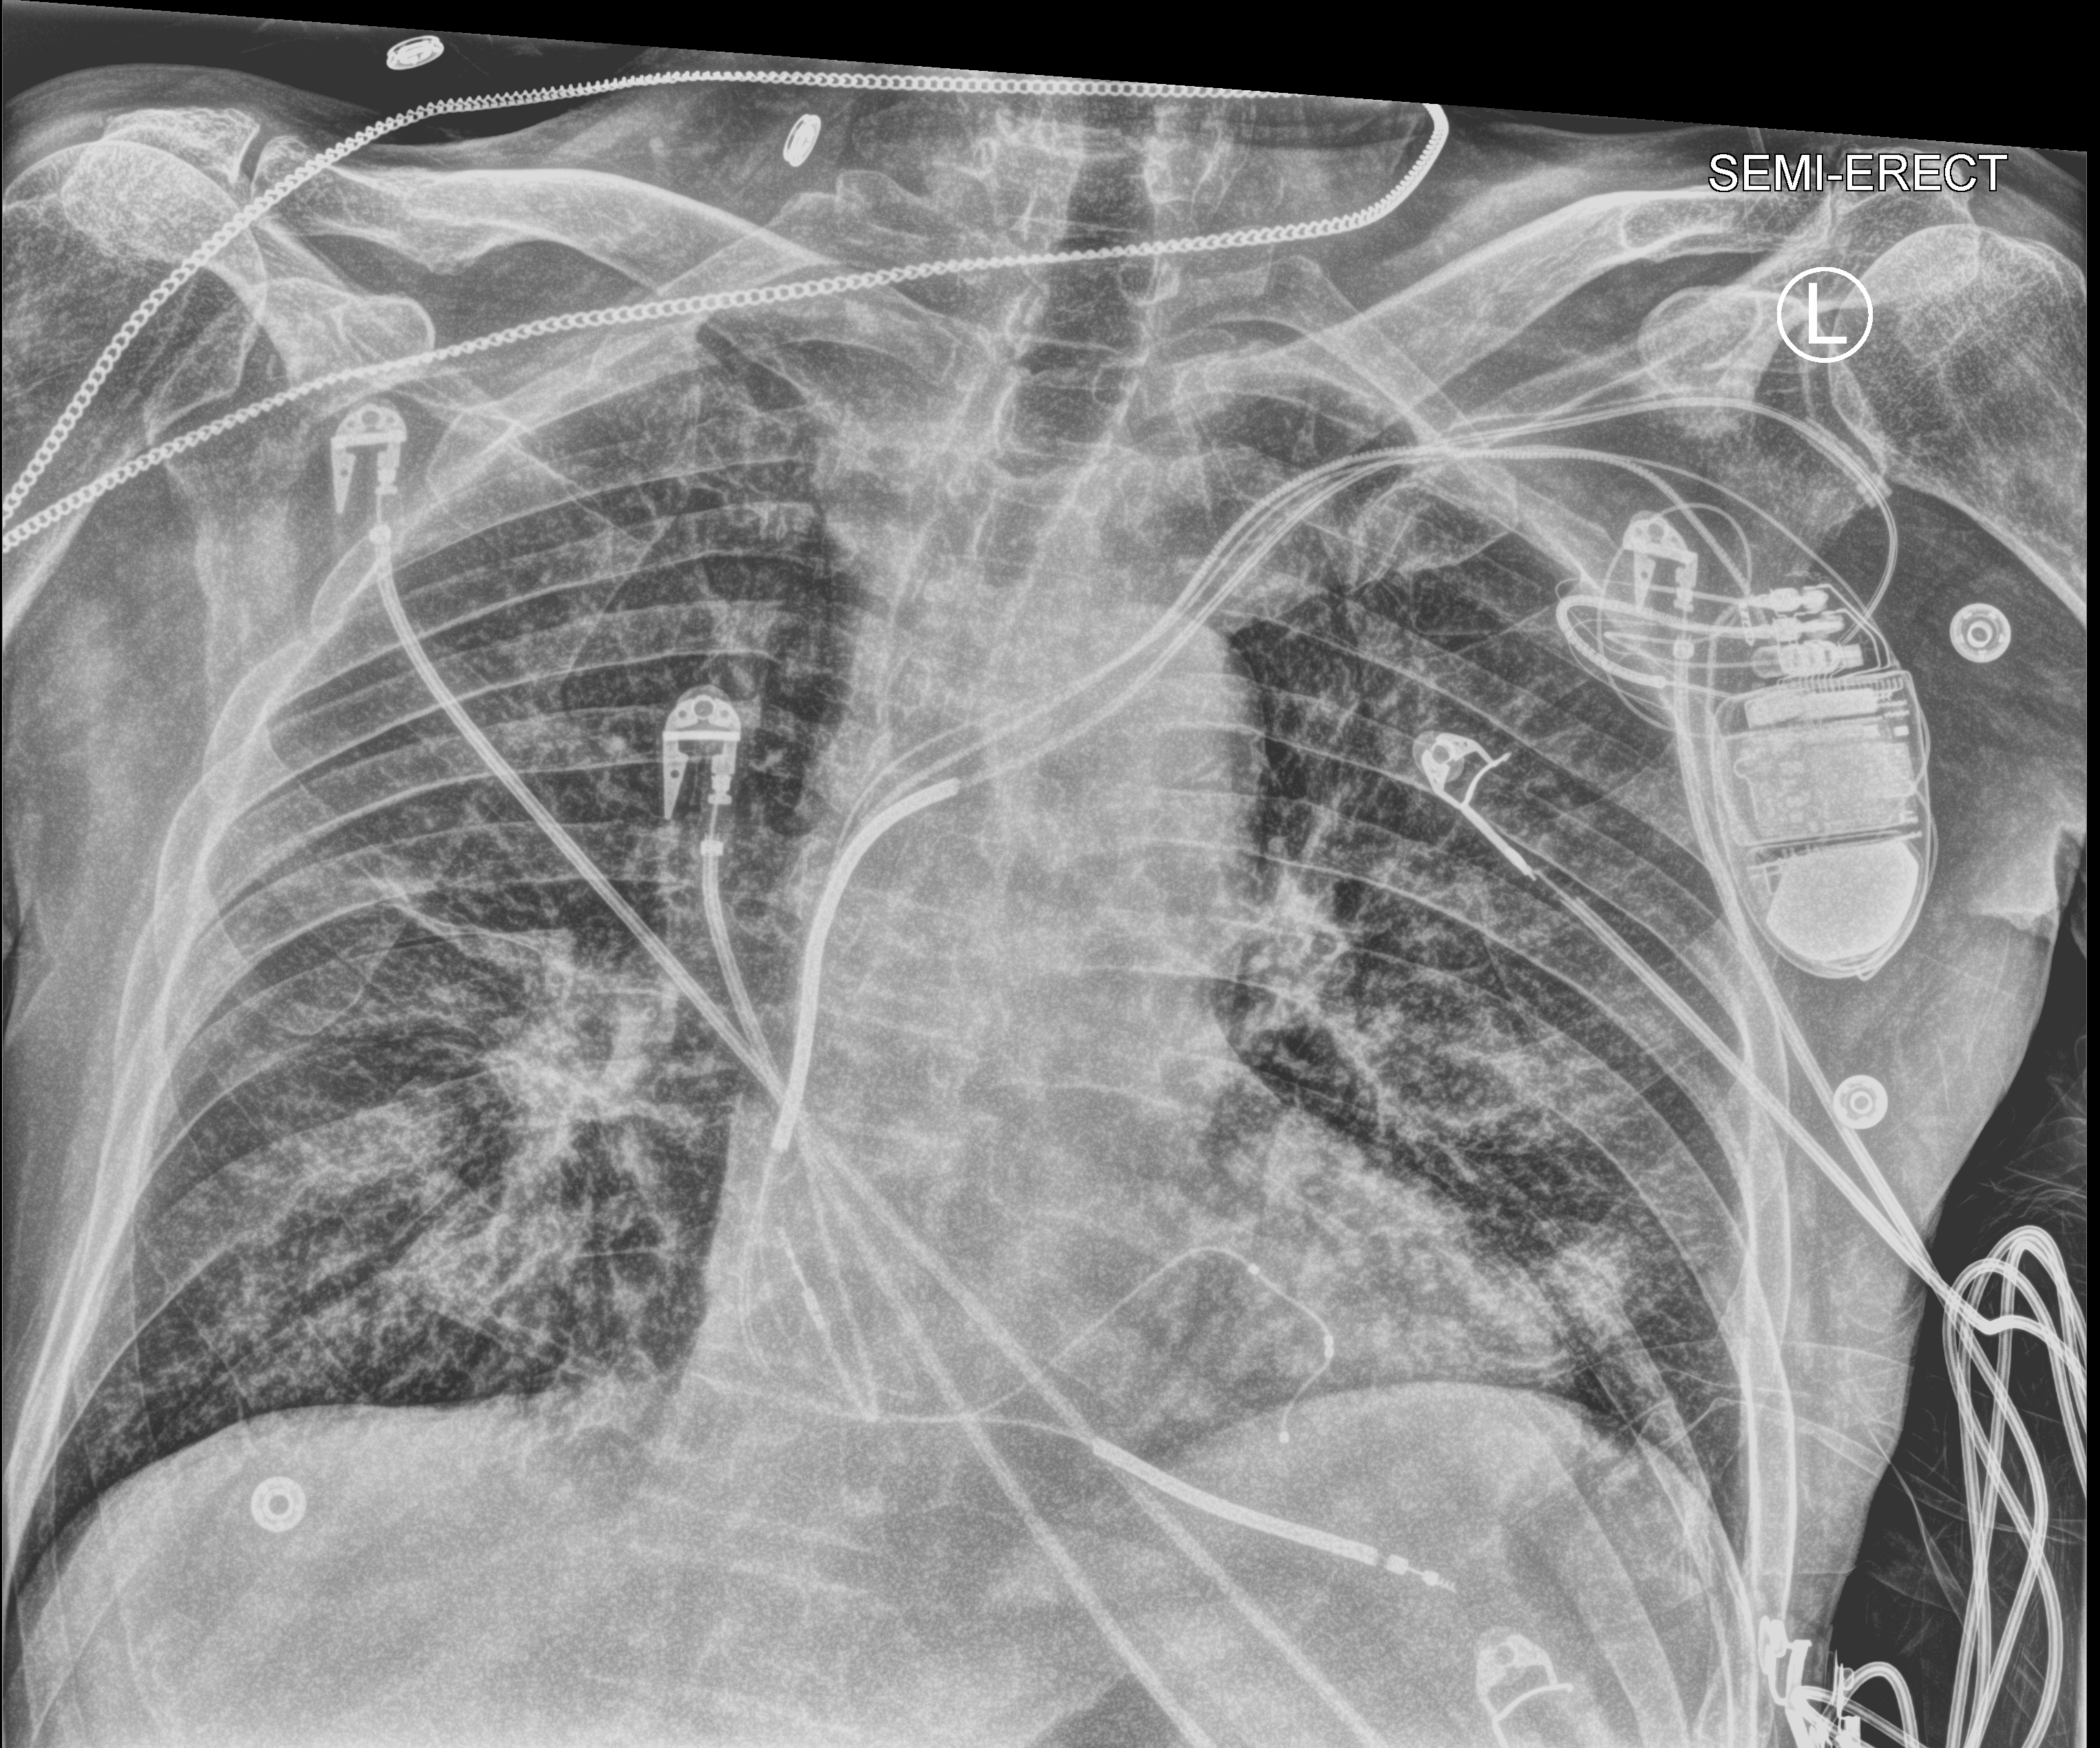
Bedside chest radiograph (computed radiography); anteroposterior (AP) projection. Patient hospitalised with COVID-19; male, aged 75–90 years.
Admission-level facts for this patient (not findings on this image; timing relative to this image not recorded): length of hospital stay: 4 days.